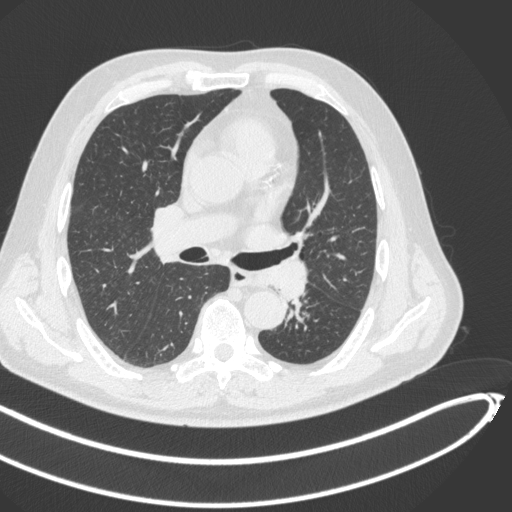
Chest CT, one axial slice; reconstruction kernel B31f; 120 kVp; lung window (W 1500 / L -600 HU); 512 × 512 image matrix, field of view 400 × 400 mm. Patient: male, 64 years. Case-level facts recorded for this patient, not image findings: clinical TNM (as recorded): T1c N0 M0; histopathological grade: G2.
Outlined on this slice (rectangle marked by the reading radiologist):
- lung tumour (recorded histology: squamous cell carcinoma): bounding box [x1, y1, x2, y2] px = [255, 261, 316, 308]